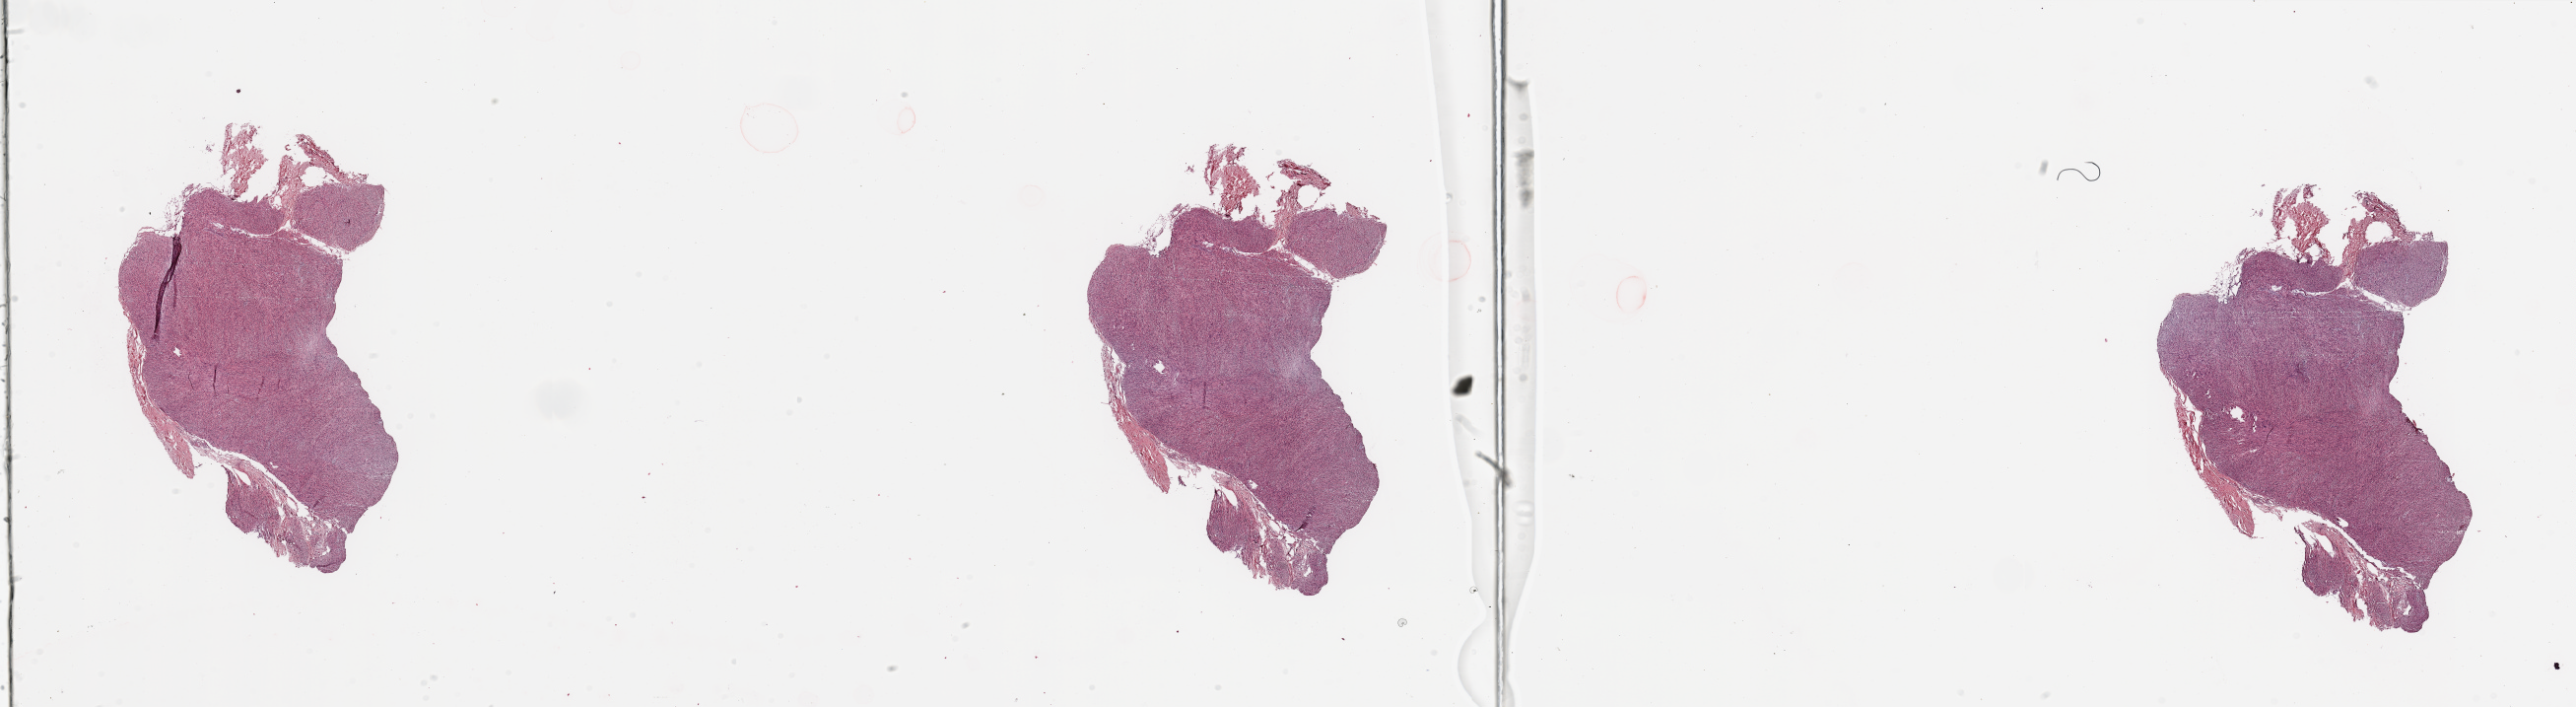
Digitized Hematoxylin and eosin (H&E) stained tissue section (whole slide), whole scanned area (about 41.3 x 11.3 mm, from a 20x scan) shown as a low-resolution overview. Tumour tissue sample. Patient: female, age 76 years.
Patient diagnosis (cohort enrolment): sarcoma (site not recorded at cohort level).